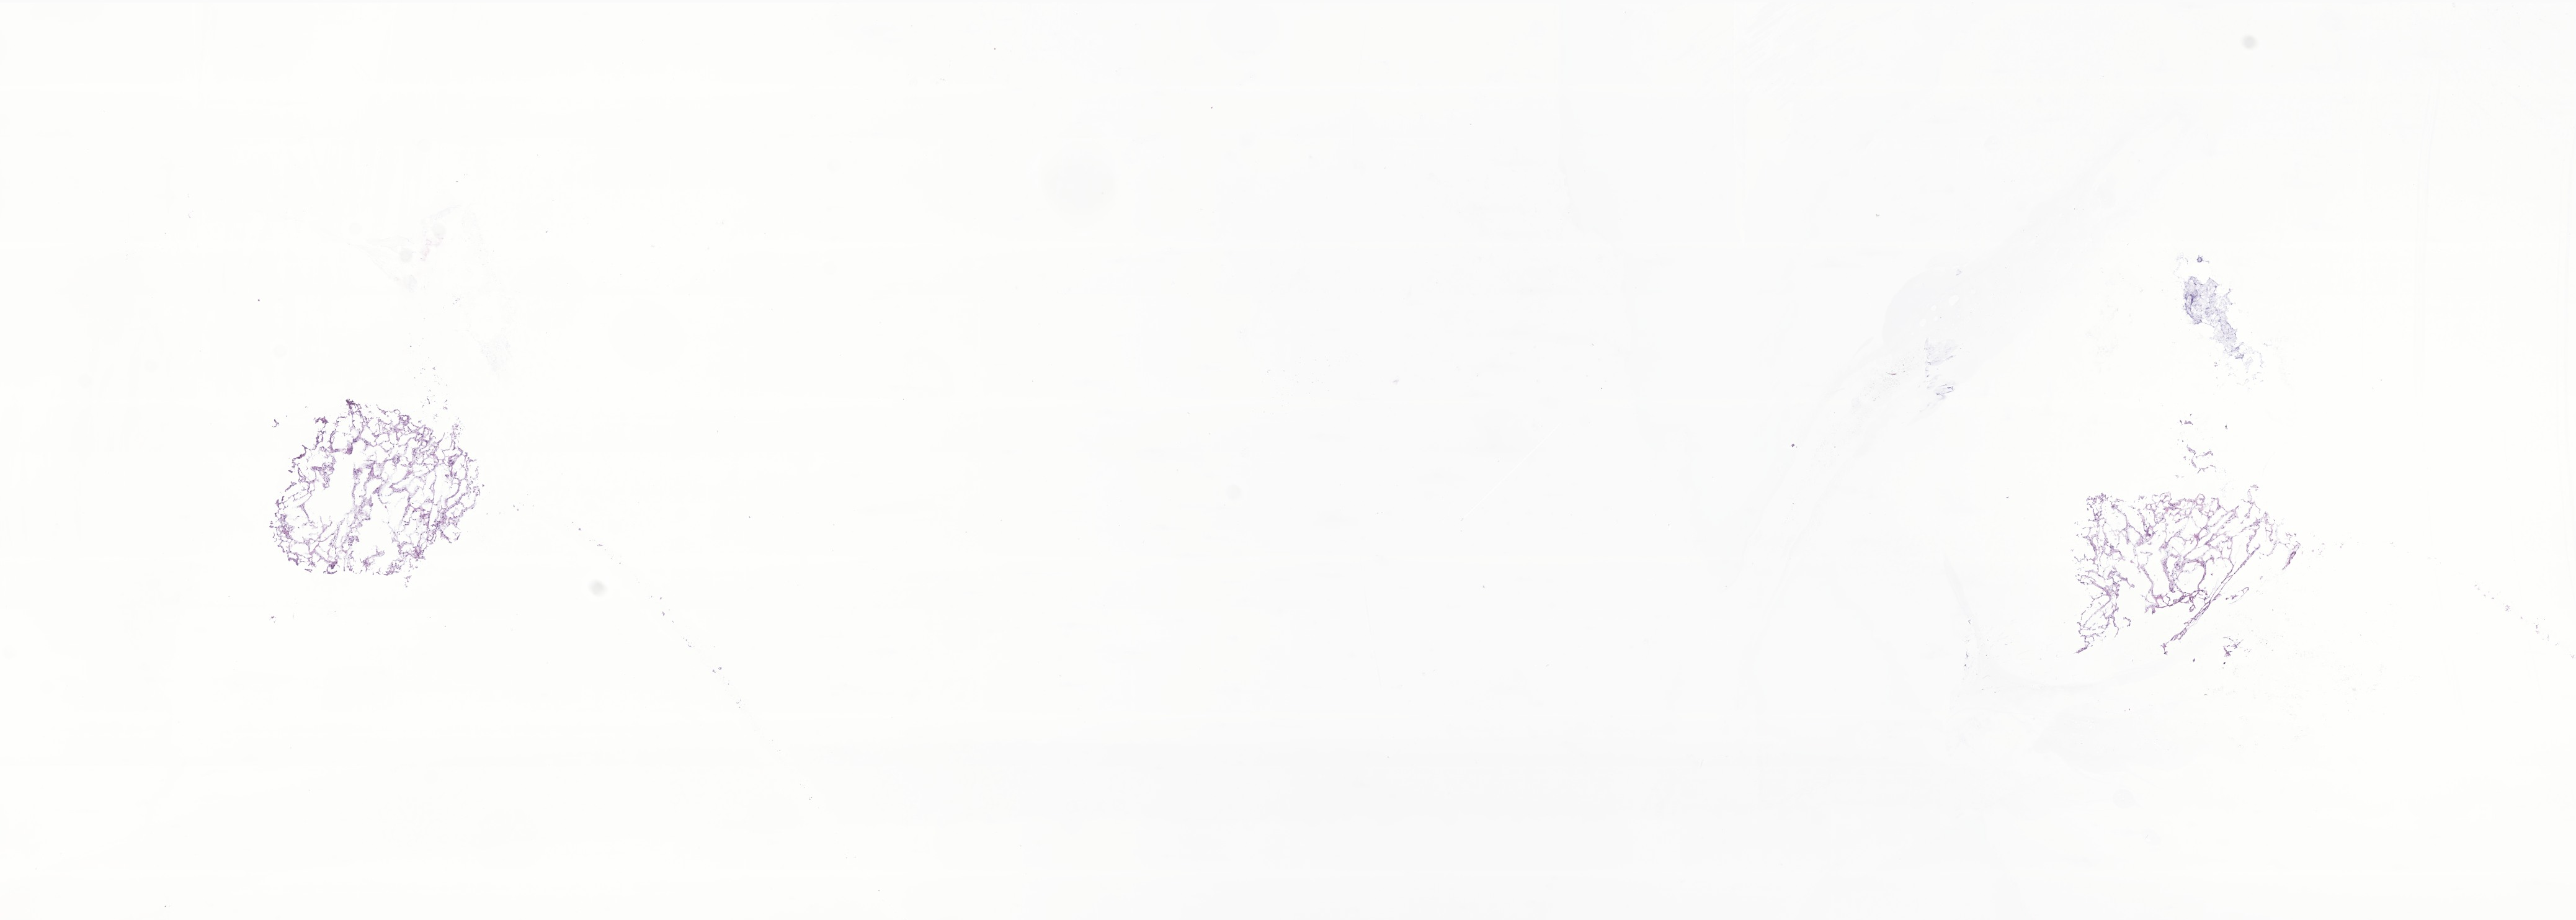
H&E whole-slide image of tumor tissue from the brain, whole scanned area (about 17.5 x 6.3 mm) shown as a low-resolution overview, cryosection (OCT / tissue freezing medium). Patient male; age 131 months (10 years 11 months).
• diagnosis: Pilocytic astrocytoma